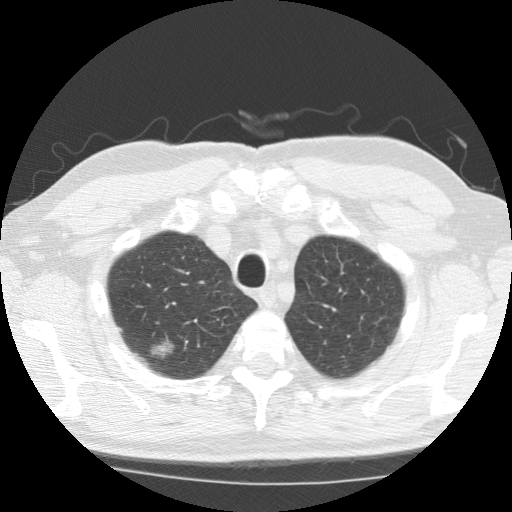
Low-dose screening chest CT, one axial slice; position 162 of 196 along the scan axis; reconstruction kernel STANDARD; lung window (W 1500 / L -600 HU); 2.5 mm slice thickness; 512 × 512 image matrix.
Annotated regions visible in this slice (expert manual segmentation):
- lesion 1 (tumor, upper lobe of right lung): box from (x=154, y=348) to (x=163, y=355) px